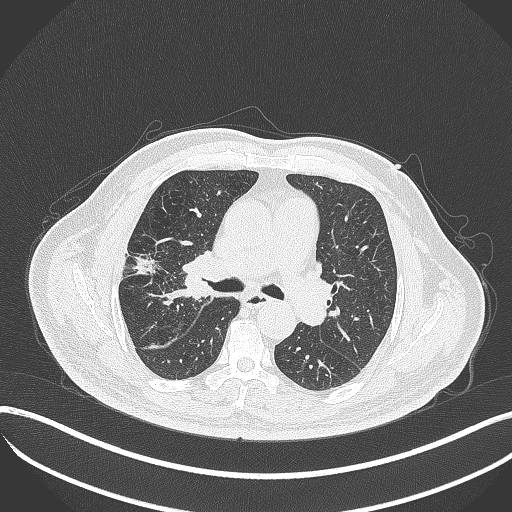
Chest CT, one axial slice; slice 220 of 401 in the series (ordered by position); reconstruction kernel B70f; 120 kVp; lung window (W 1500 / L -600 HU); 1 mm slice thickness; 512 × 512 image matrix, field of view 400 × 400 mm. Male patient, age 72 years. From the clinical record (not read from this slice): clinical TNM (as recorded): T1c N0 M0.
Structures marked on this image (bounding box drawn by a radiologist):
- lung tumour (recorded histology: squamous cell carcinoma): bounding box <162,250,201,310> (left, top, right, bottom; pixels)